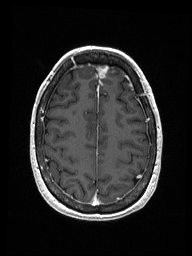
Brain MRI from a brain-tumour surgery series, one axial slice; position 46 of 192 along the scan axis; T1-weighted post-contrast; 1 mm slice thickness; 192 × 256 image matrix, field of view 187 × 250 mm. Case-level facts recorded for this patient, not image findings: histopathology: Metastastic Carcinoma from Breast primary.
Structures marked on this image (manually delineated by an expert):
- previous resection cavity: bounding box (x1, y1, x2, y2) in pixels: (97, 65, 109, 79)